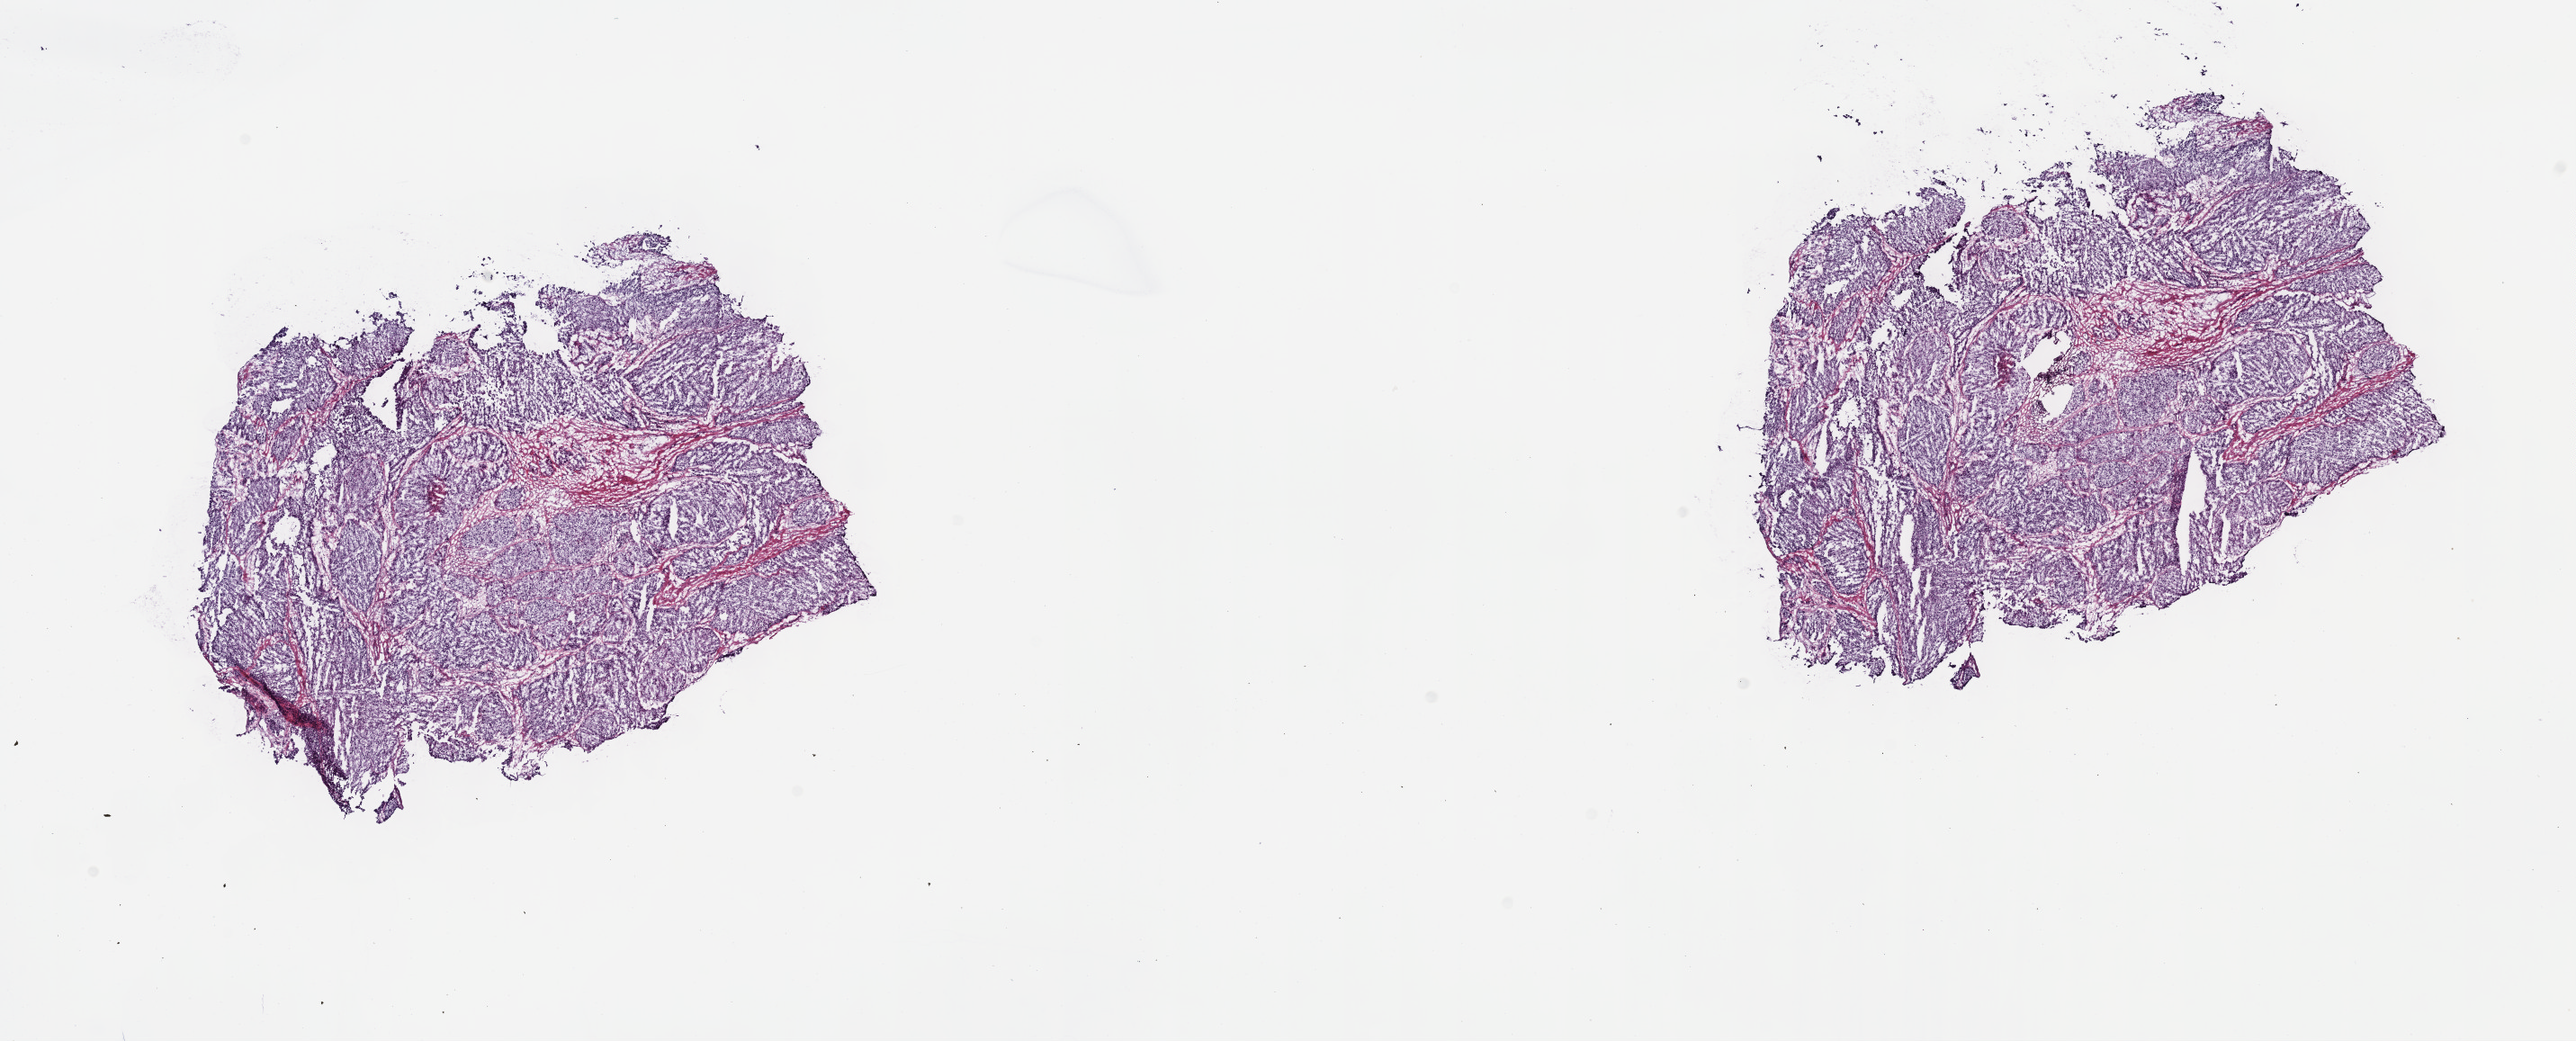
Whole-slide histology image, Hematoxylin and eosin (H&E) stained — shown as a low-resolution overview of the whole scanned area (about 23.2 x 9.4 mm, slide scanned at 40x); frozen section from the top of the tissue portion; bladder, primary tumour sample. Male patient; age at initial diagnosis 69 years. Histologic grade: high grade. Composition of this section per pathologist review: tumour cells 80%, tumour nuclei 90%, normal cells 0%, stromal cells 20%, necrosis 0%. Inflammatory infiltration, as recorded: lymphocyte infiltration 0%, monocyte infiltration 0%, neutrophil infiltration 0%.
* pathologic diagnosis: Transitional cell carcinoma
* AJCC pathologic stage: III